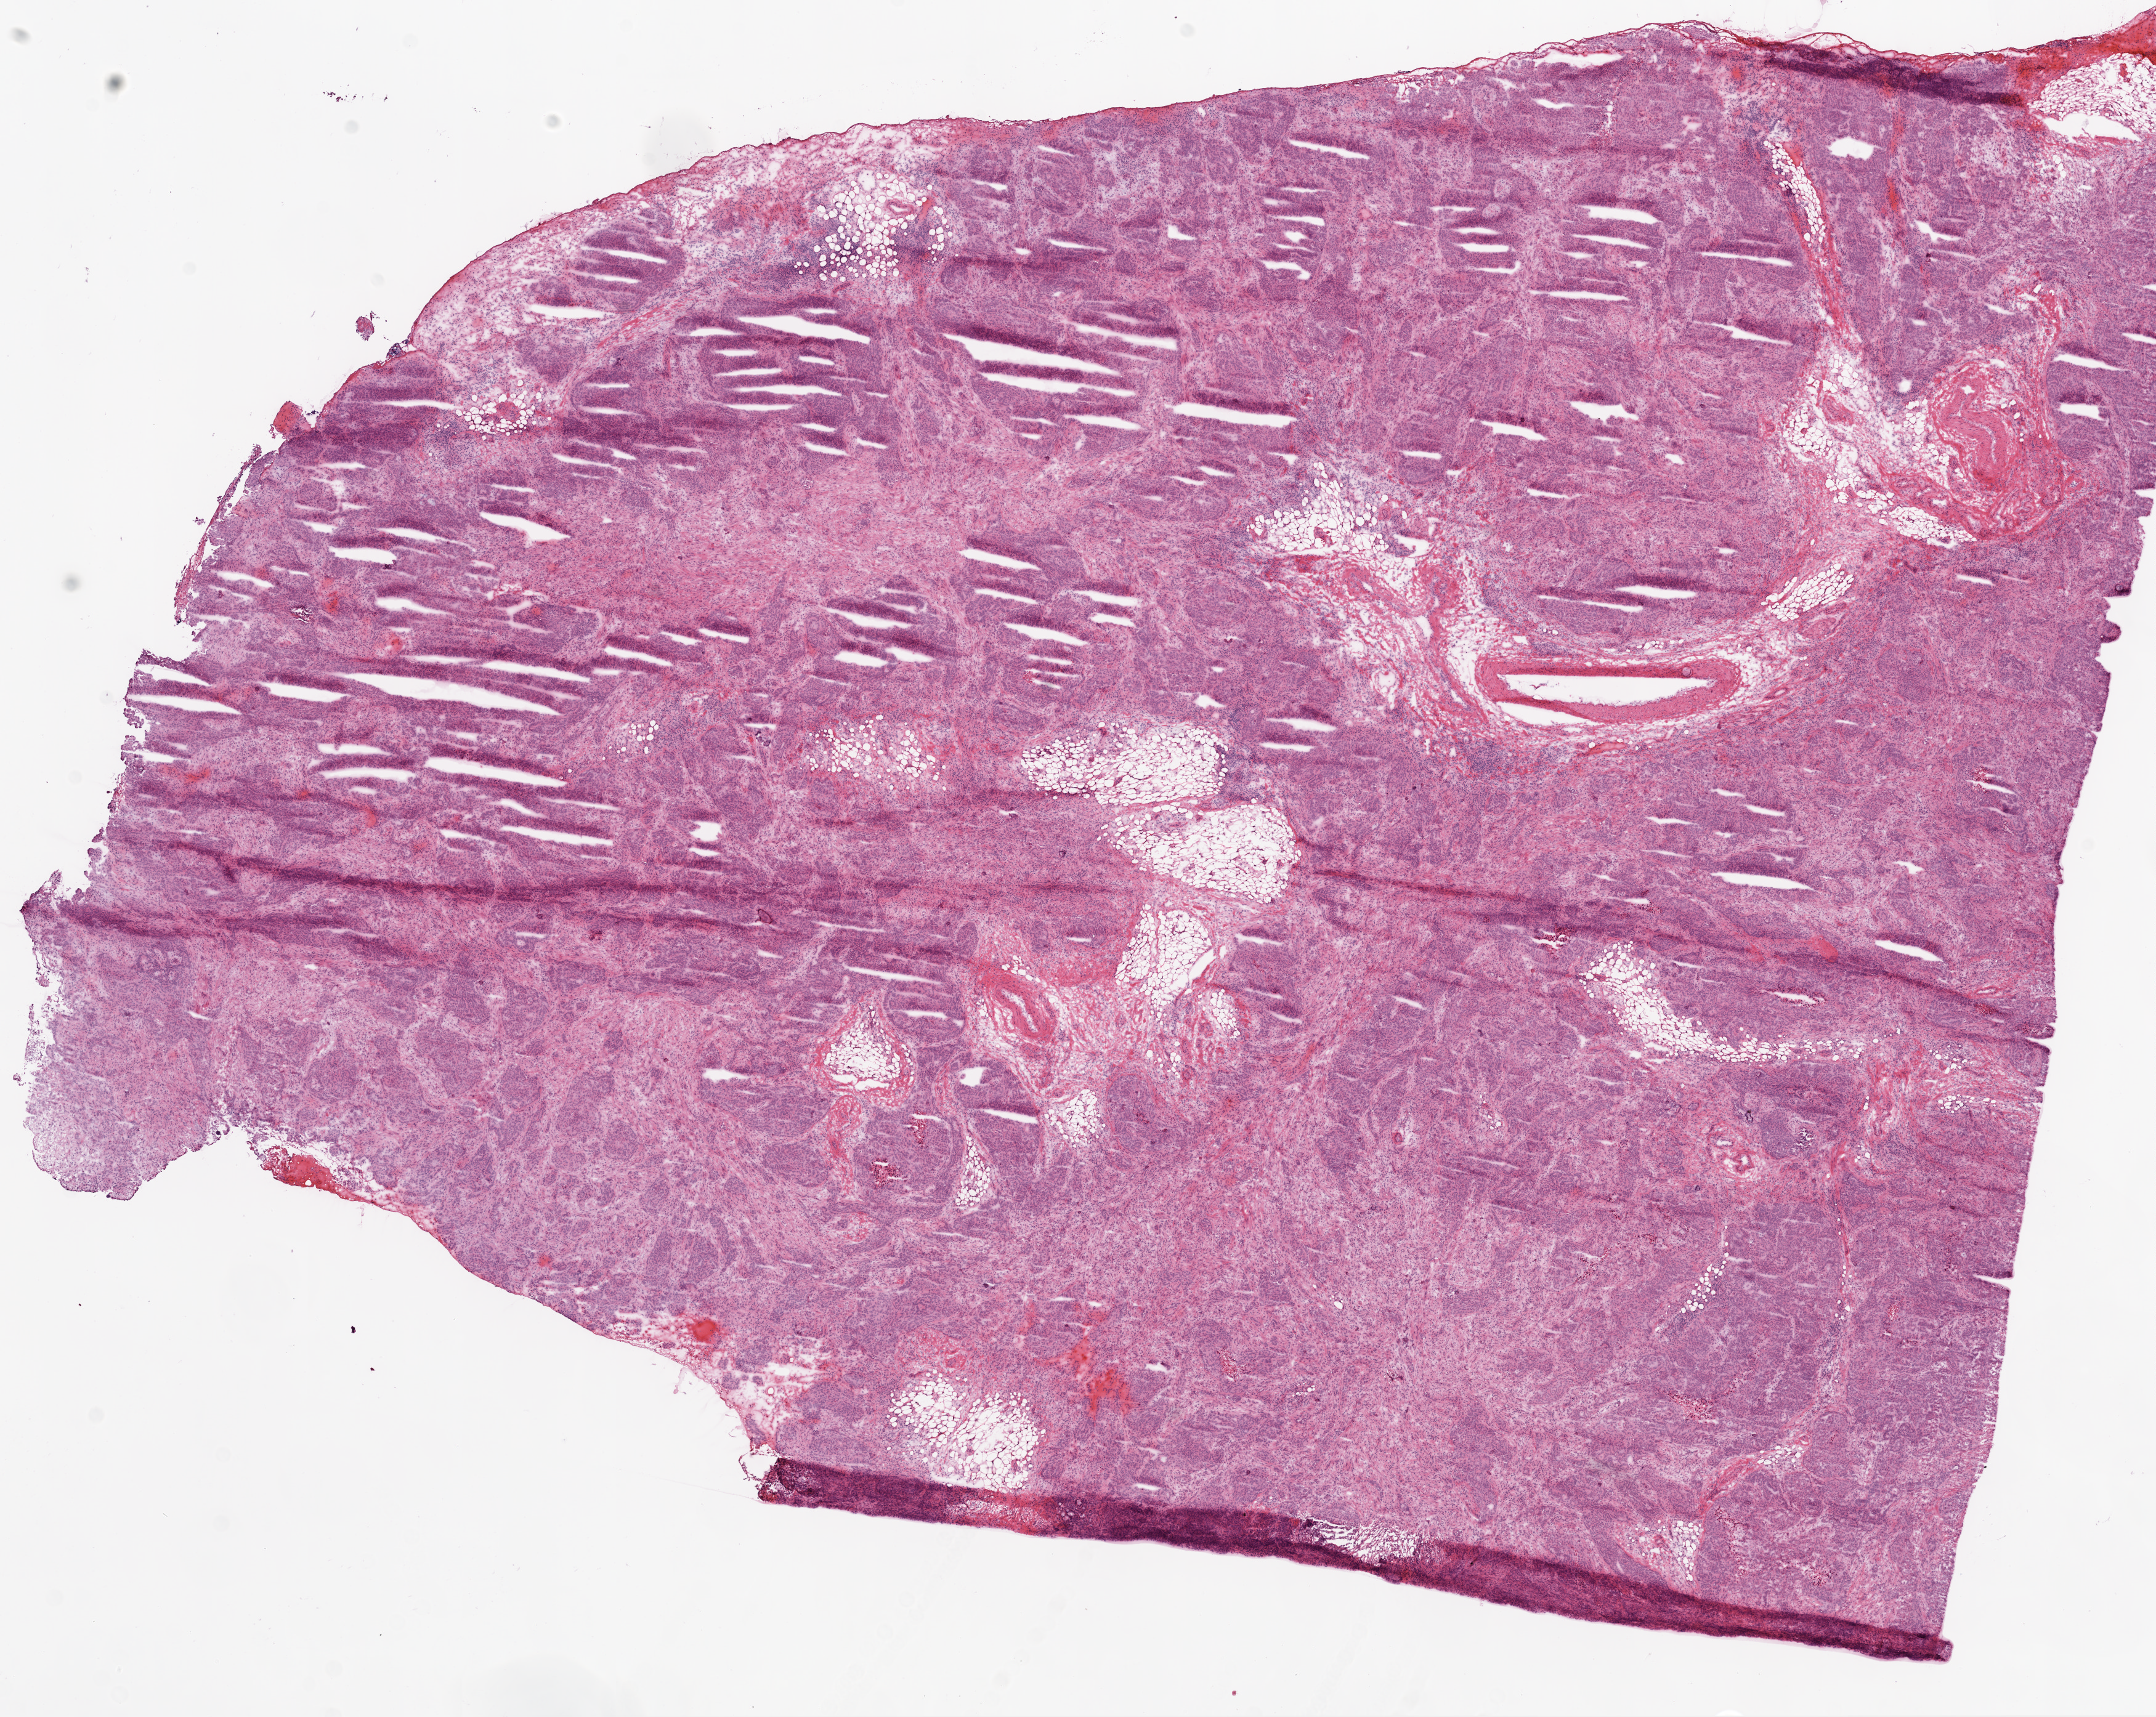
Whole-slide histology image, H&E-stained — whole scanned area (about 14.0 x 11.2 mm, acquisition: 20x scan) shown as a low-resolution overview, frozen section from the top of the tissue portion, primary tumour sample from the ovary. Female patient; age at initial diagnosis 64 years.
Pathologic diagnosis: Serous cystadenocarcinoma, NOS.